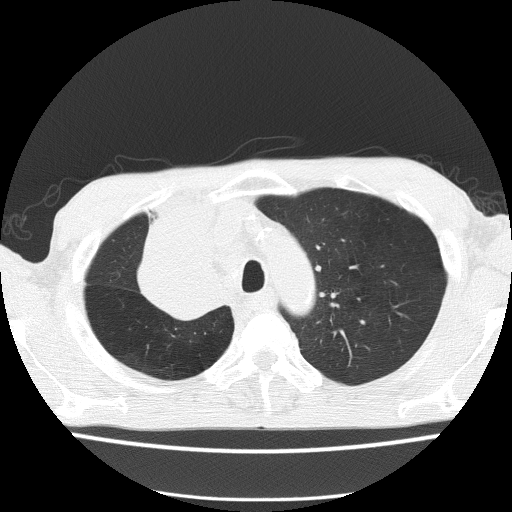
Low-dose screening chest CT, one axial slice; slice 117 of 150 in the series (ordered by position); 120 kVp; lung window (W 1500 / L -600 HU); 2 mm slice thickness; 512 × 512 image matrix, field of view 336 × 336 mm.
Outlined on this slice (manually delineated by an expert):
- lesion 1 (tumor, hilum of right lung): bounding box [x1, y1, x2, y2] px = [139, 200, 221, 318]